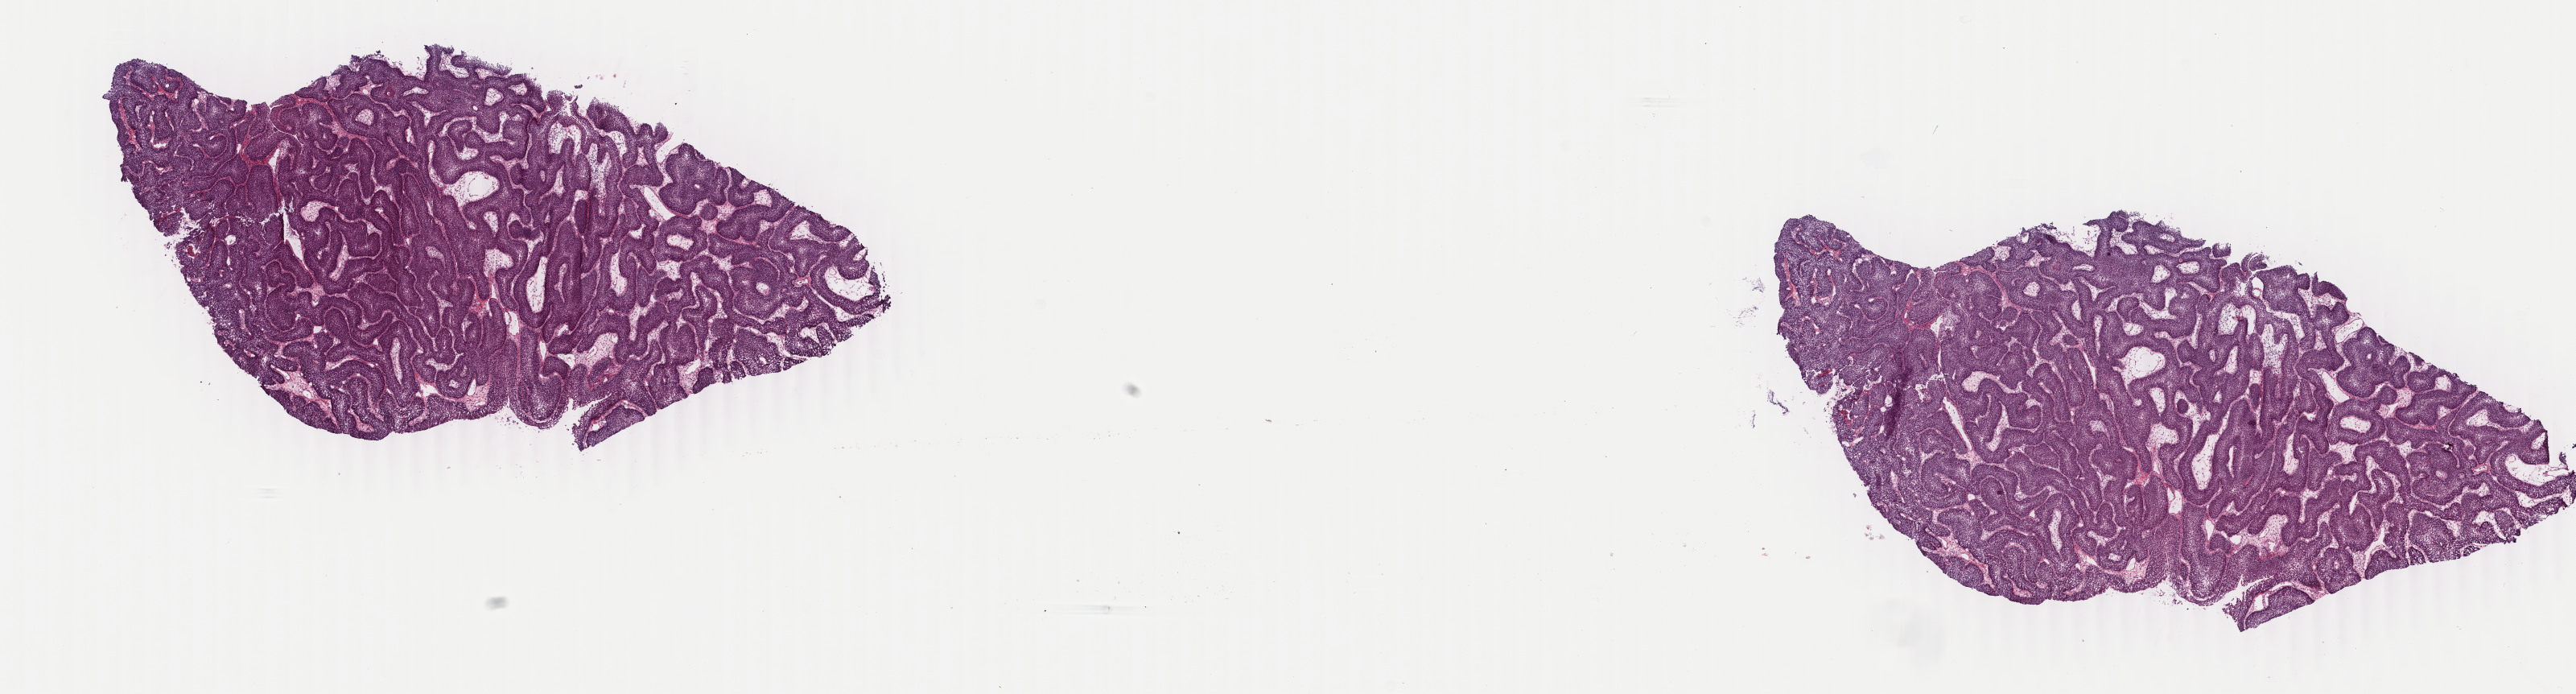
Whole-slide histology image, H&E, shown as a low-resolution overview of the whole scanned area (about 25.5 x 6.9 mm, from a 40x scan). Frozen section. Primary tumour sample from the bladder. Male, age 37 years at initial diagnosis. Histologic grade: low grade. Slide review estimates, as recorded: tumour cells 90%, tumour nuclei 90%, normal cells 5%, stromal cells 5%, necrosis 0%. Inflammatory infiltration, as recorded: lymphocyte infiltration 2%, monocyte infiltration 2%, neutrophil infiltration 0%.
AJCC pathologic stage: II (7th edition). Pathologic diagnosis: Papillary transitional cell carcinoma.